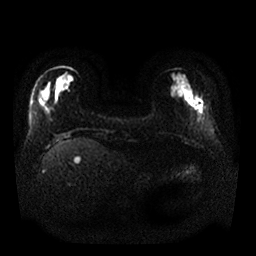
Breast MRI, one axial slice. Position 7 of 25 along the scan axis. Diffusion-weighted series; image 2 of 4 stored at this slice position (different b-values; order by instance number). 1.5 T. 256 × 256 image matrix, field of view 340 × 340 mm. Female patient.
Structures marked on this image (outlined manually by an expert reader):
- tumour on diffusion-weighted imaging: box from (x=194, y=95) to (x=206, y=114) px